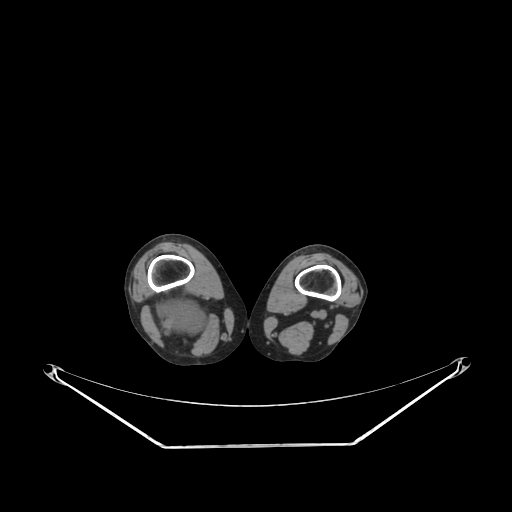
CT of an extremity soft-tissue mass (from a PET/CT study), one axial slice. Position 185 of 267 along the scan axis. 140 kVp. Soft-tissue window (W 400 / L 40 HU). 512 × 512 image matrix. Female patient. From the clinical record (not read from this slice): histological type: liposarcoma; site of the primary tumour: right thigh.
Outlined on this slice (expert contour drawn on MRI and transferred to this co-registered scan by the dataset authors):
- gross tumour volume (mass): bounding box <155,297,209,337> (left, top, right, bottom; pixels)